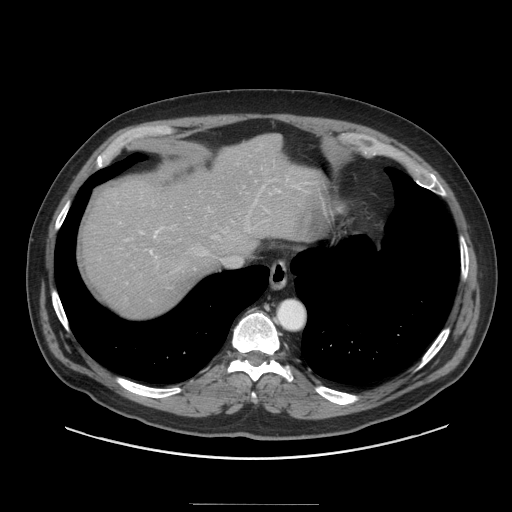
Contrast-enhanced abdominal CT (liver protocol), one axial slice; slice 78 of 91 in the series (ordered by position); soft-tissue window (W 400 / L 40 HU); 512 × 512 image matrix. Case-level facts recorded for this patient, not image findings: diagnosis: hepatocellular carcinoma (patient treated with transarterial chemoembolisation; whether this scan precedes or follows treatment is not stated here); TNM stage (as recorded): Stage-I; Child-Pugh class: A; tumour differentiation: well differentiated; tumour size: 4 cm.
Structures marked on this image (semi-automatic segmentation, software-assisted and operator-edited):
- liver parenchyma outside the tumour (the mass and vessels are separate outlines, so this box may not span the whole liver): bounding box [x1, y1, x2, y2] px = [80, 134, 328, 316]
- liver vessels: [126, 227, 163, 254]